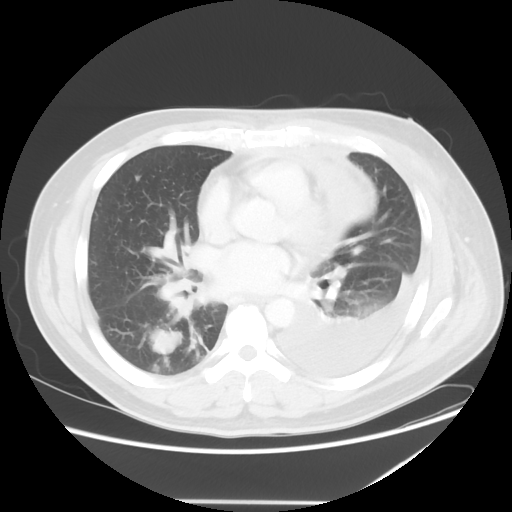
Chest CT, one axial slice; position 25 of 52 along the scan axis; lung window (W 1500 / L -600 HU); 5 mm slice thickness; 512 × 512 image matrix. Patient: male, 42 years. From the clinical record (not read from this slice): clinical TNM (as recorded): T2 N1 M1.
Structures marked on this image (rectangle marked by the reading radiologist):
- lung tumour (recorded histology: adenocarcinoma): bounding box [x1, y1, x2, y2] px = [142, 321, 189, 362]